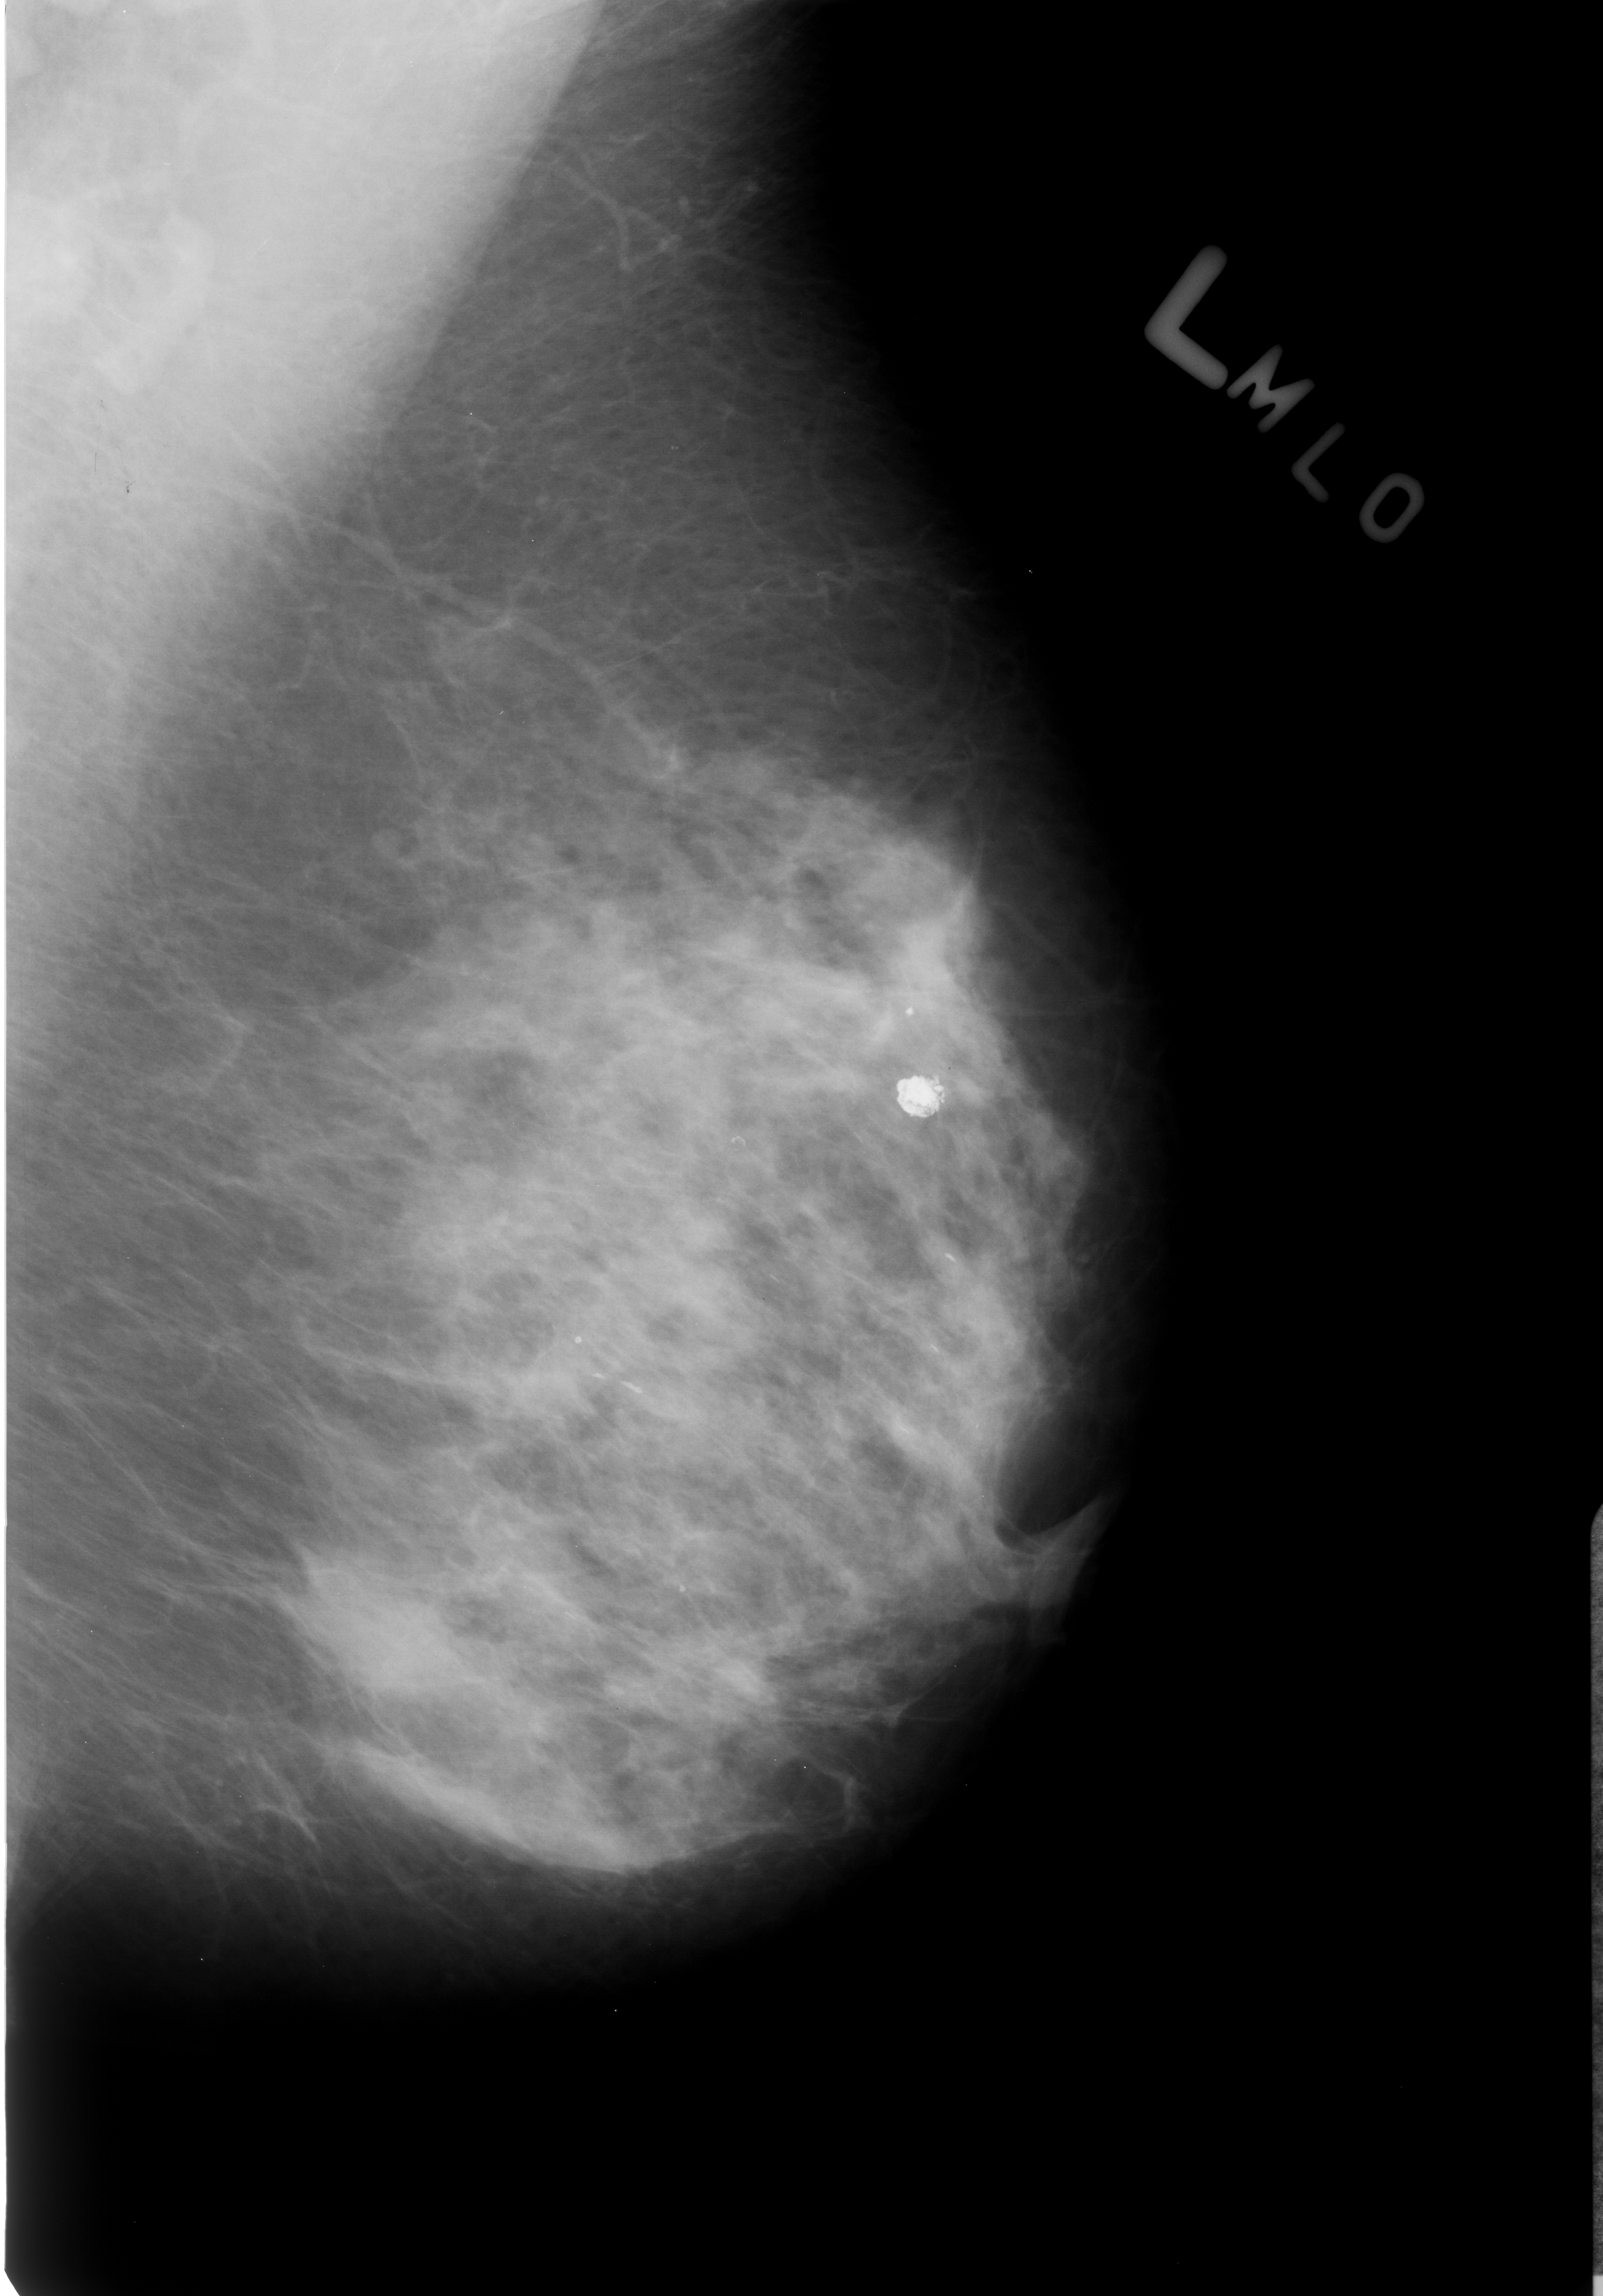
Scanned film-screen mammogram, left breast, MLO view, breast composition: heterogeneously dense (BI-RADS density category 3 of 4).
Marked findings (only marked abnormalities are described; nothing is implied about the rest of the image): calcifications, distribution linear; BI-RADS assessment category 2; subtlety rating 3 on a 1 (subtle) to 5 (obvious) scale; benign without callback (not worked up further).